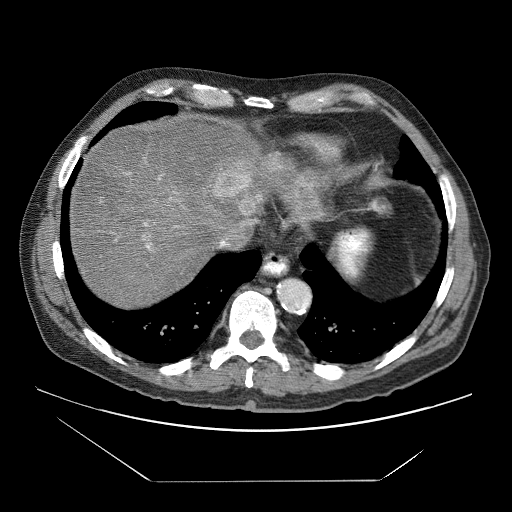
Contrast-enhanced abdominal CT (liver protocol), one axial slice. 120 kVp. Soft-tissue window (W 400 / L 40 HU). 2.5 mm slice thickness. 512 × 512 image matrix. From the clinical record (not read from this slice): diagnosis: hepatocellular carcinoma (patient treated with transarterial chemoembolisation; whether this scan precedes or follows treatment is not stated here); TNM stage (as recorded): Stage-IVB; Child-Pugh class: B; tumour differentiation: poorly differentiated; tumour nodularity: uninodular.
Annotated regions visible in this slice (semi-automatic segmentation, software-assisted and operator-edited):
- liver parenchyma outside the tumour (the mass and vessels are separate outlines, so this box may not span the whole liver): bounding box [x1, y1, x2, y2] px = [70, 114, 318, 306]
- mass: [212, 153, 324, 226]
- liver vessels: [127, 173, 251, 251]